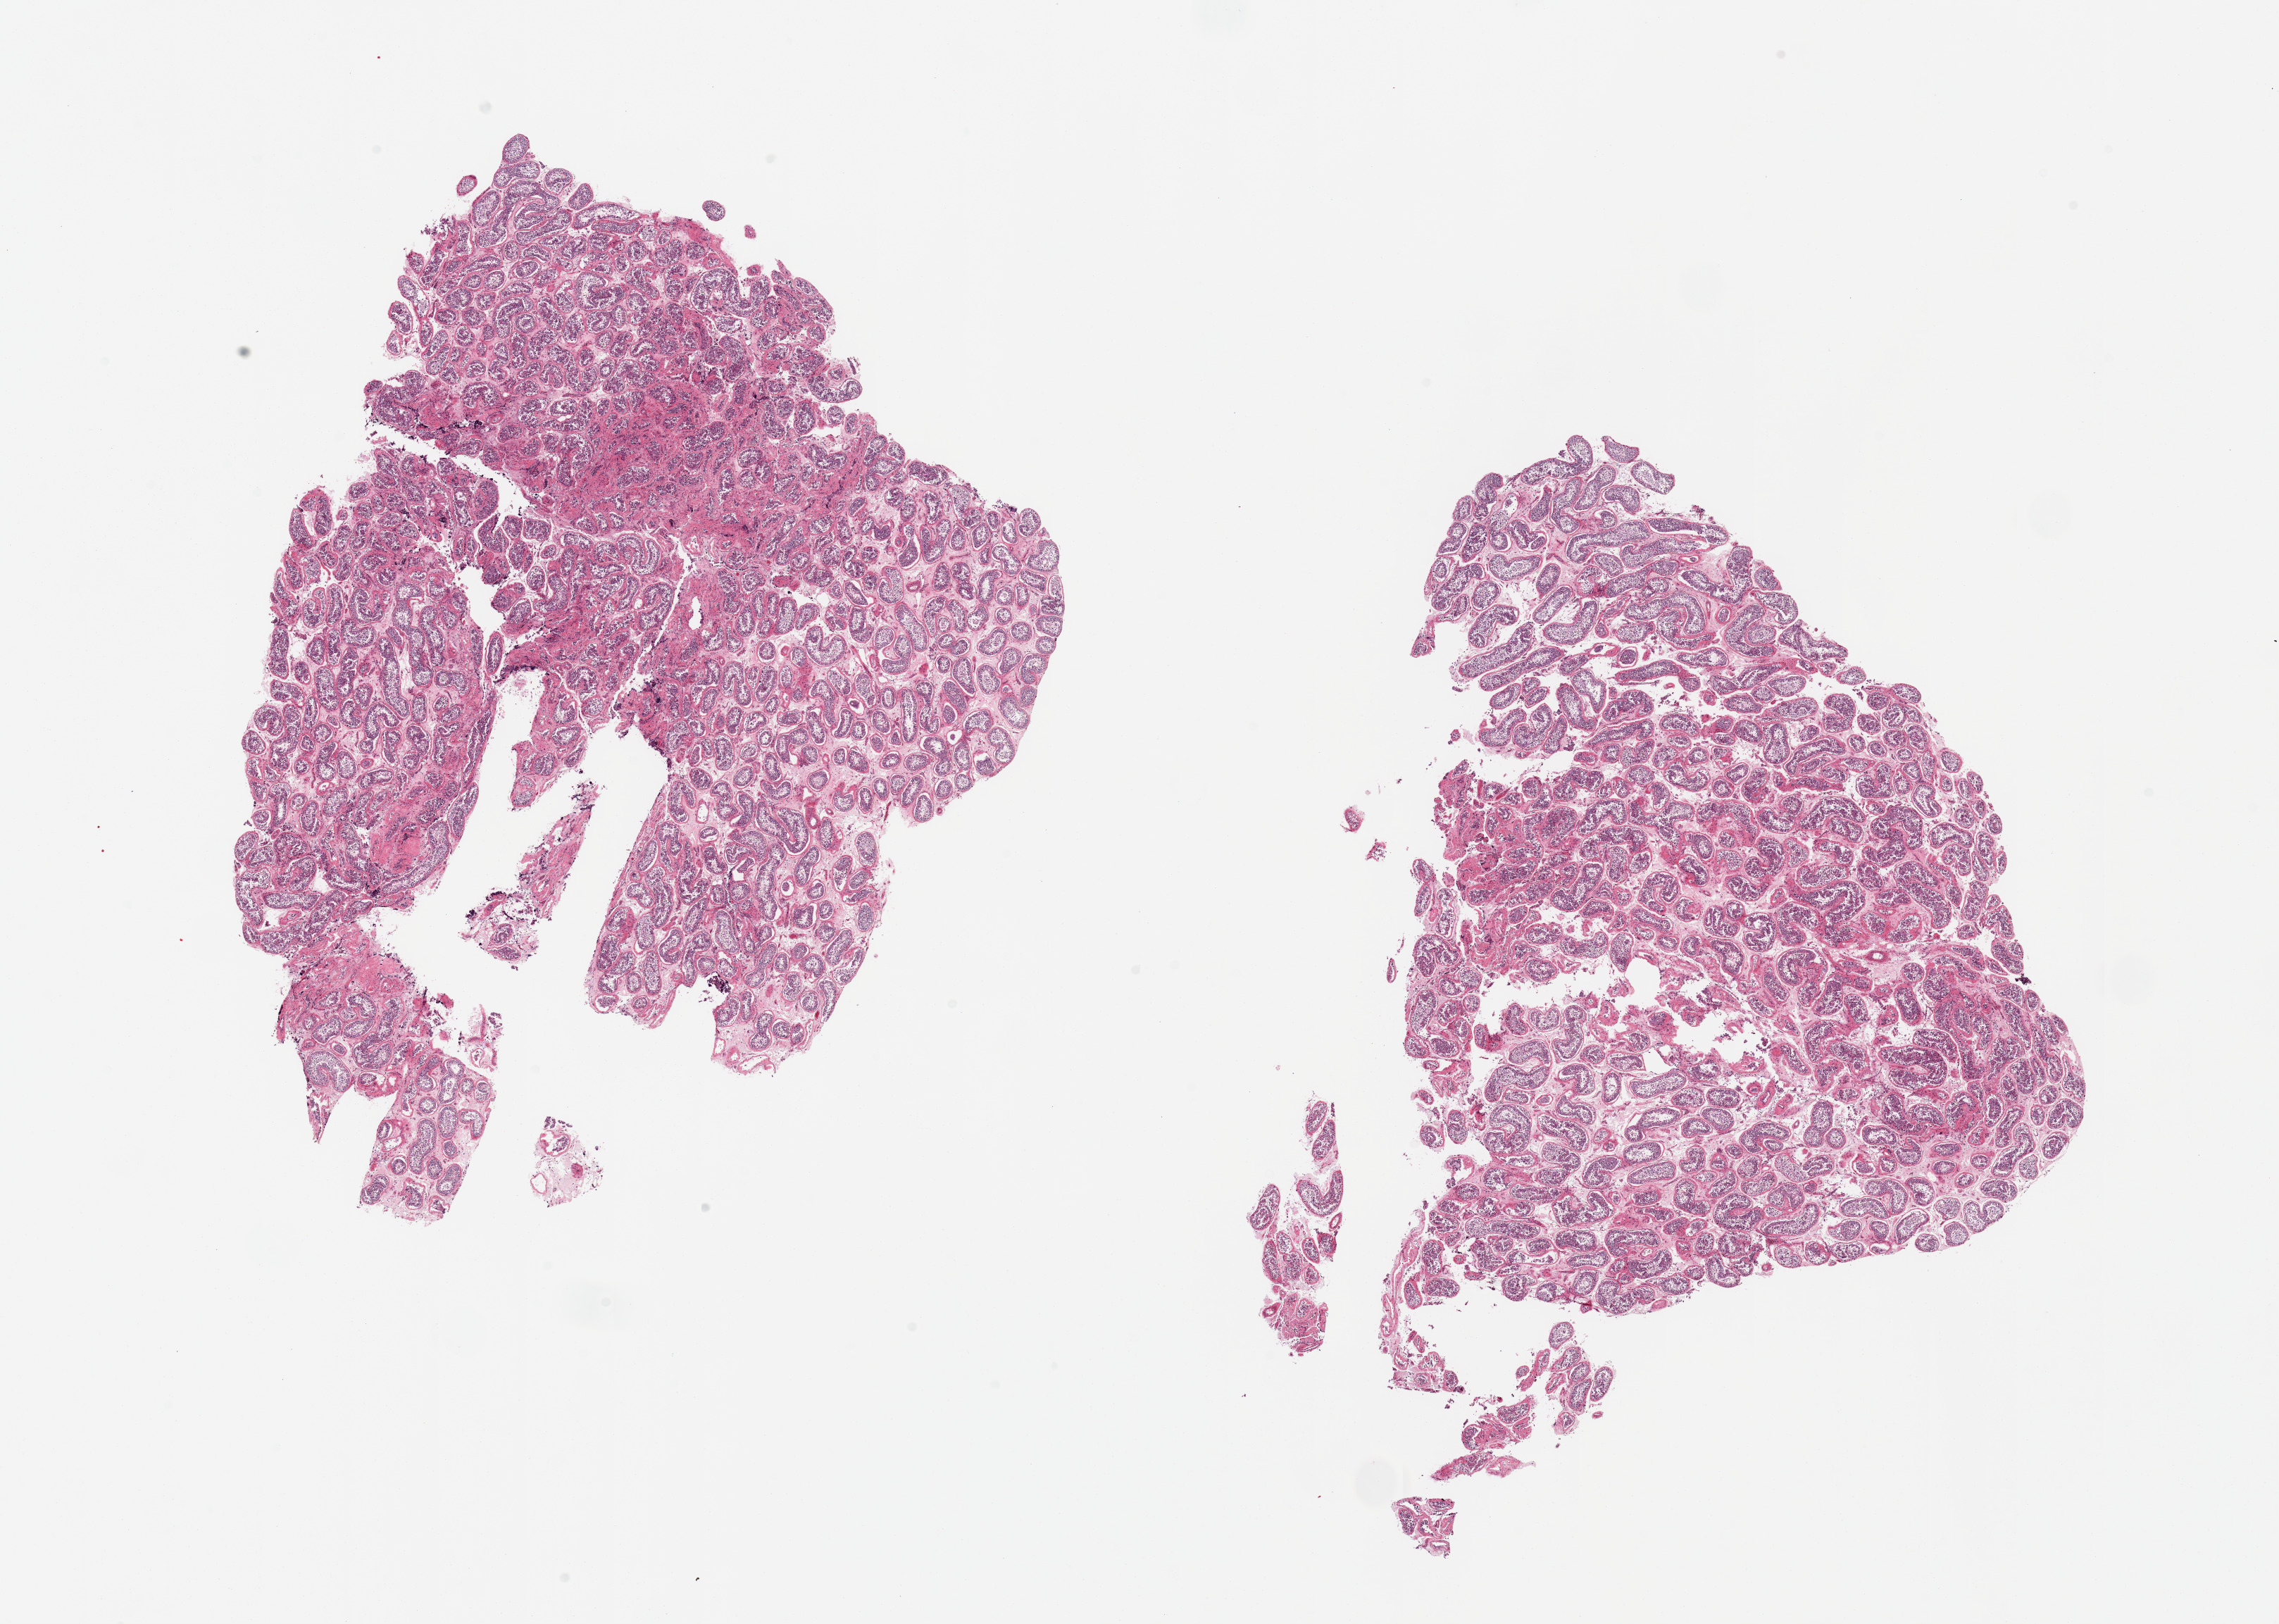
Haematoxylin and eosin whole-slide image, brightfield, a low-resolution overview of the entire scanned area, about 25.6 x 18.2 mm. PAXgene-fixed paraffin-embedded (PFPE) section. Sampled site (target tissue): testis. Donor tissue sample. Male donor.
* reviewer comment on this tissue sample: 2 pieces; spermatogenesis is present